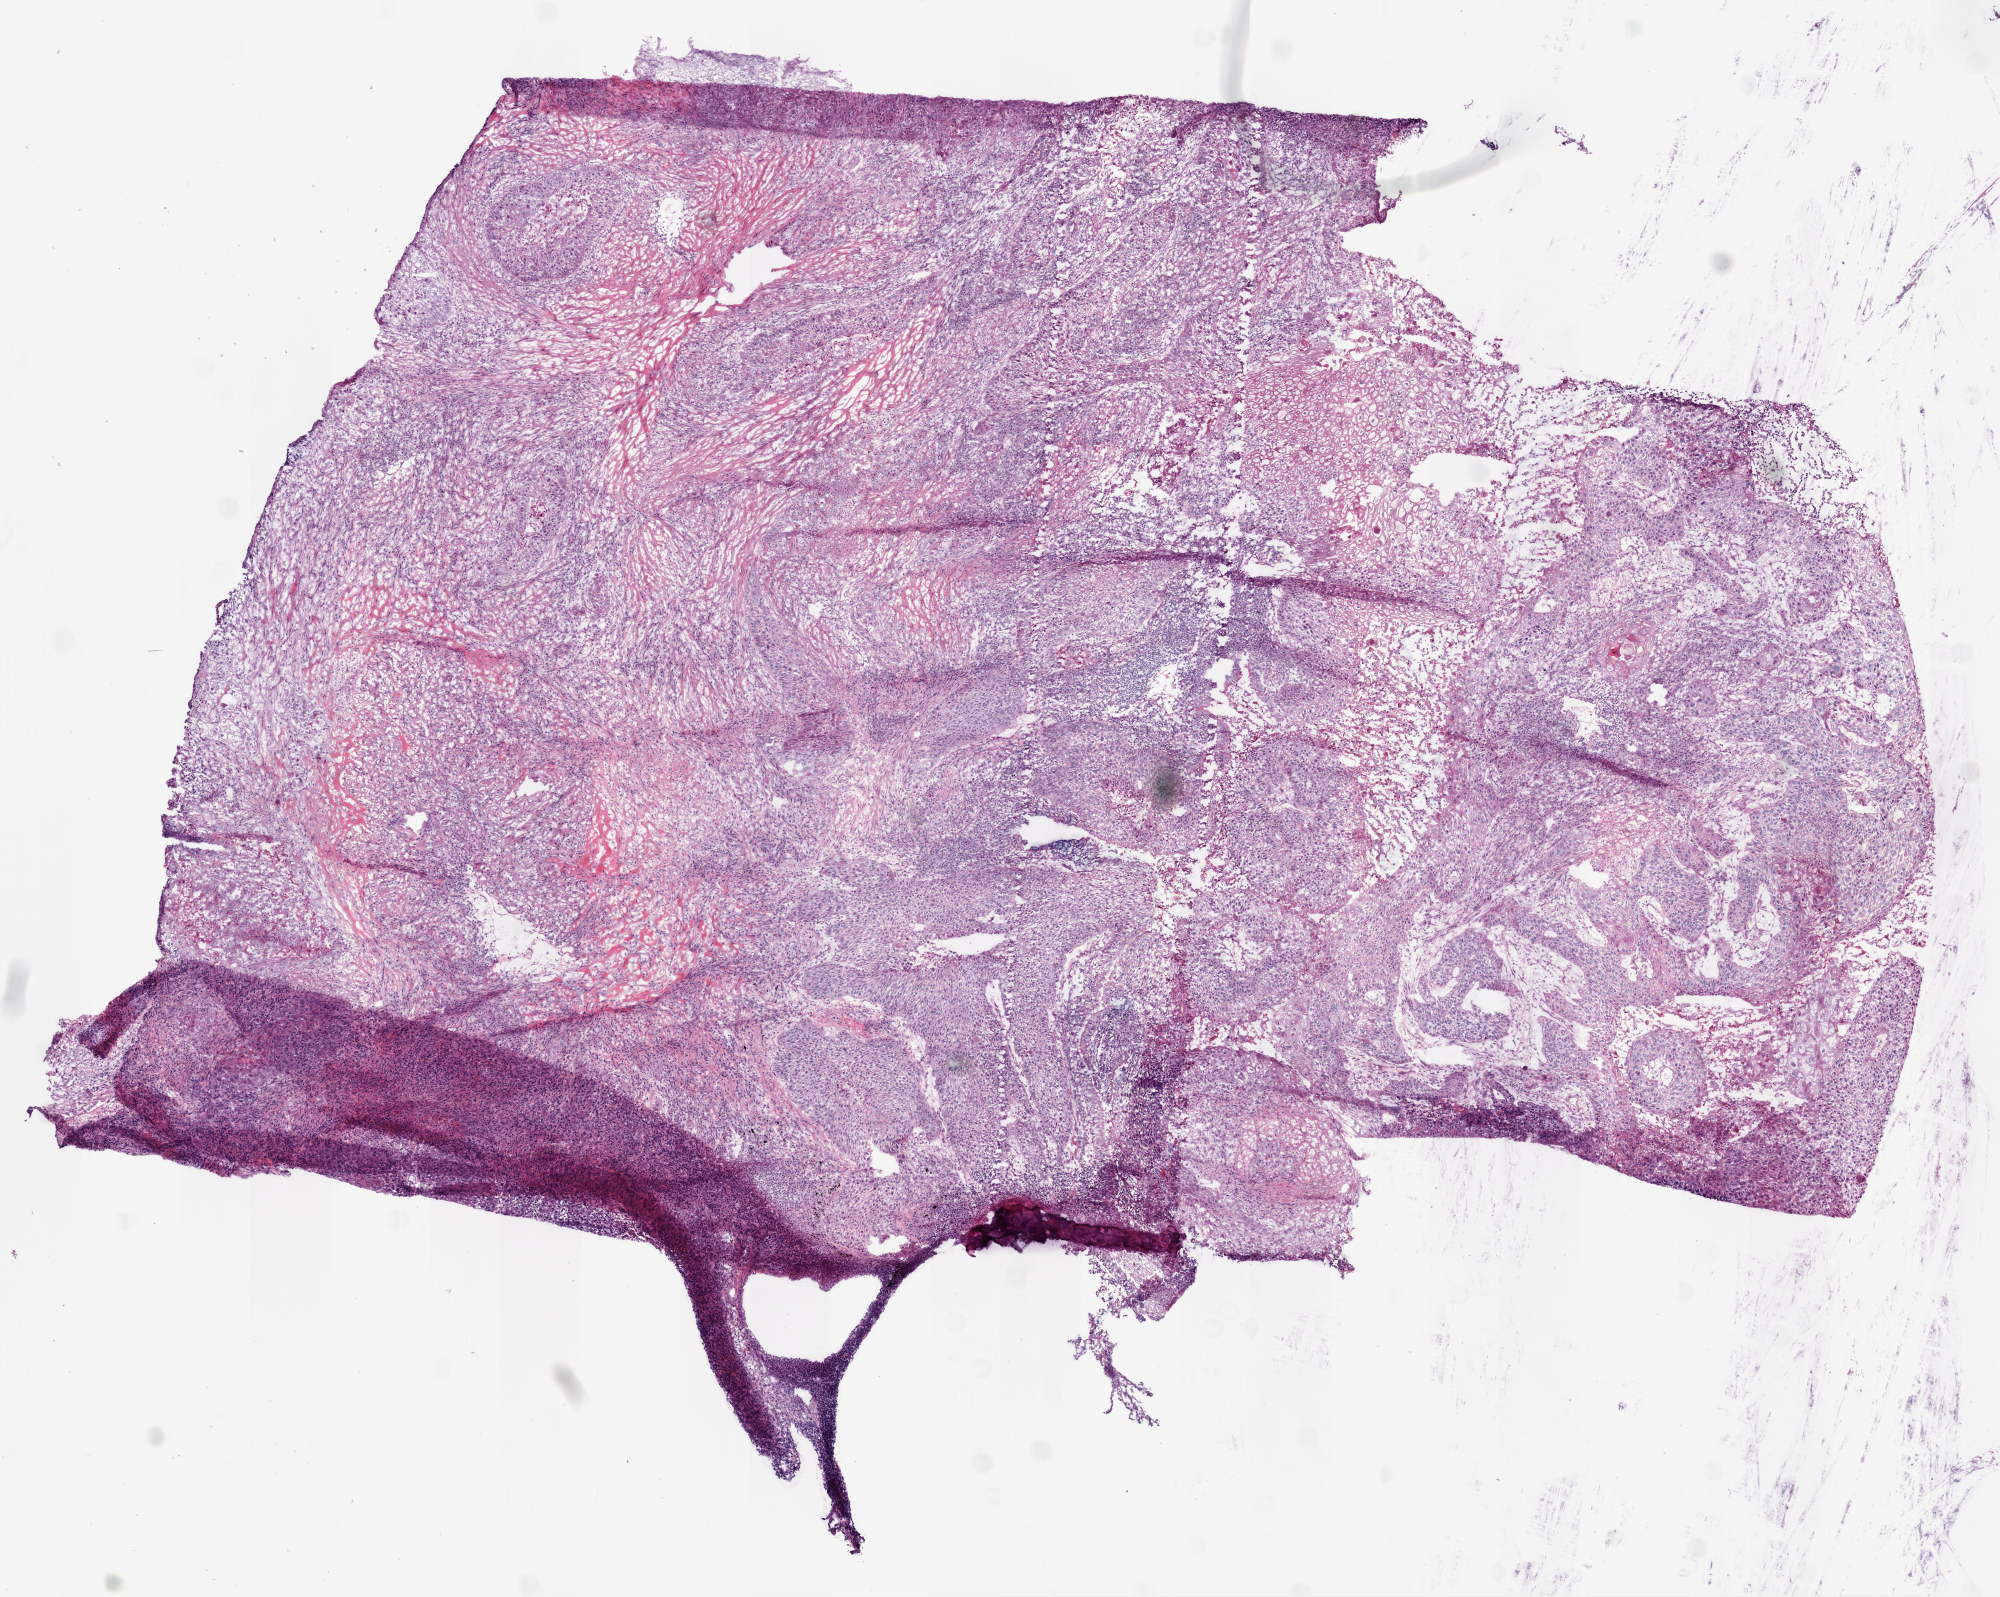
Digitized Hematoxylin and eosin (H&E) stained tissue section (whole slide), shown as a low-resolution overview of the whole scanned area (about 8.0 x 6.4 mm, from a 20x scan), frozen section, primary tumour sample from the lung. Patient: male, age at initial diagnosis 56 years. Composition of this section per pathologist review: tumour cells 76%, tumour nuclei 75%.
Pathologic diagnosis: Squamous cell carcinoma, NOS (lower lobe, lung).